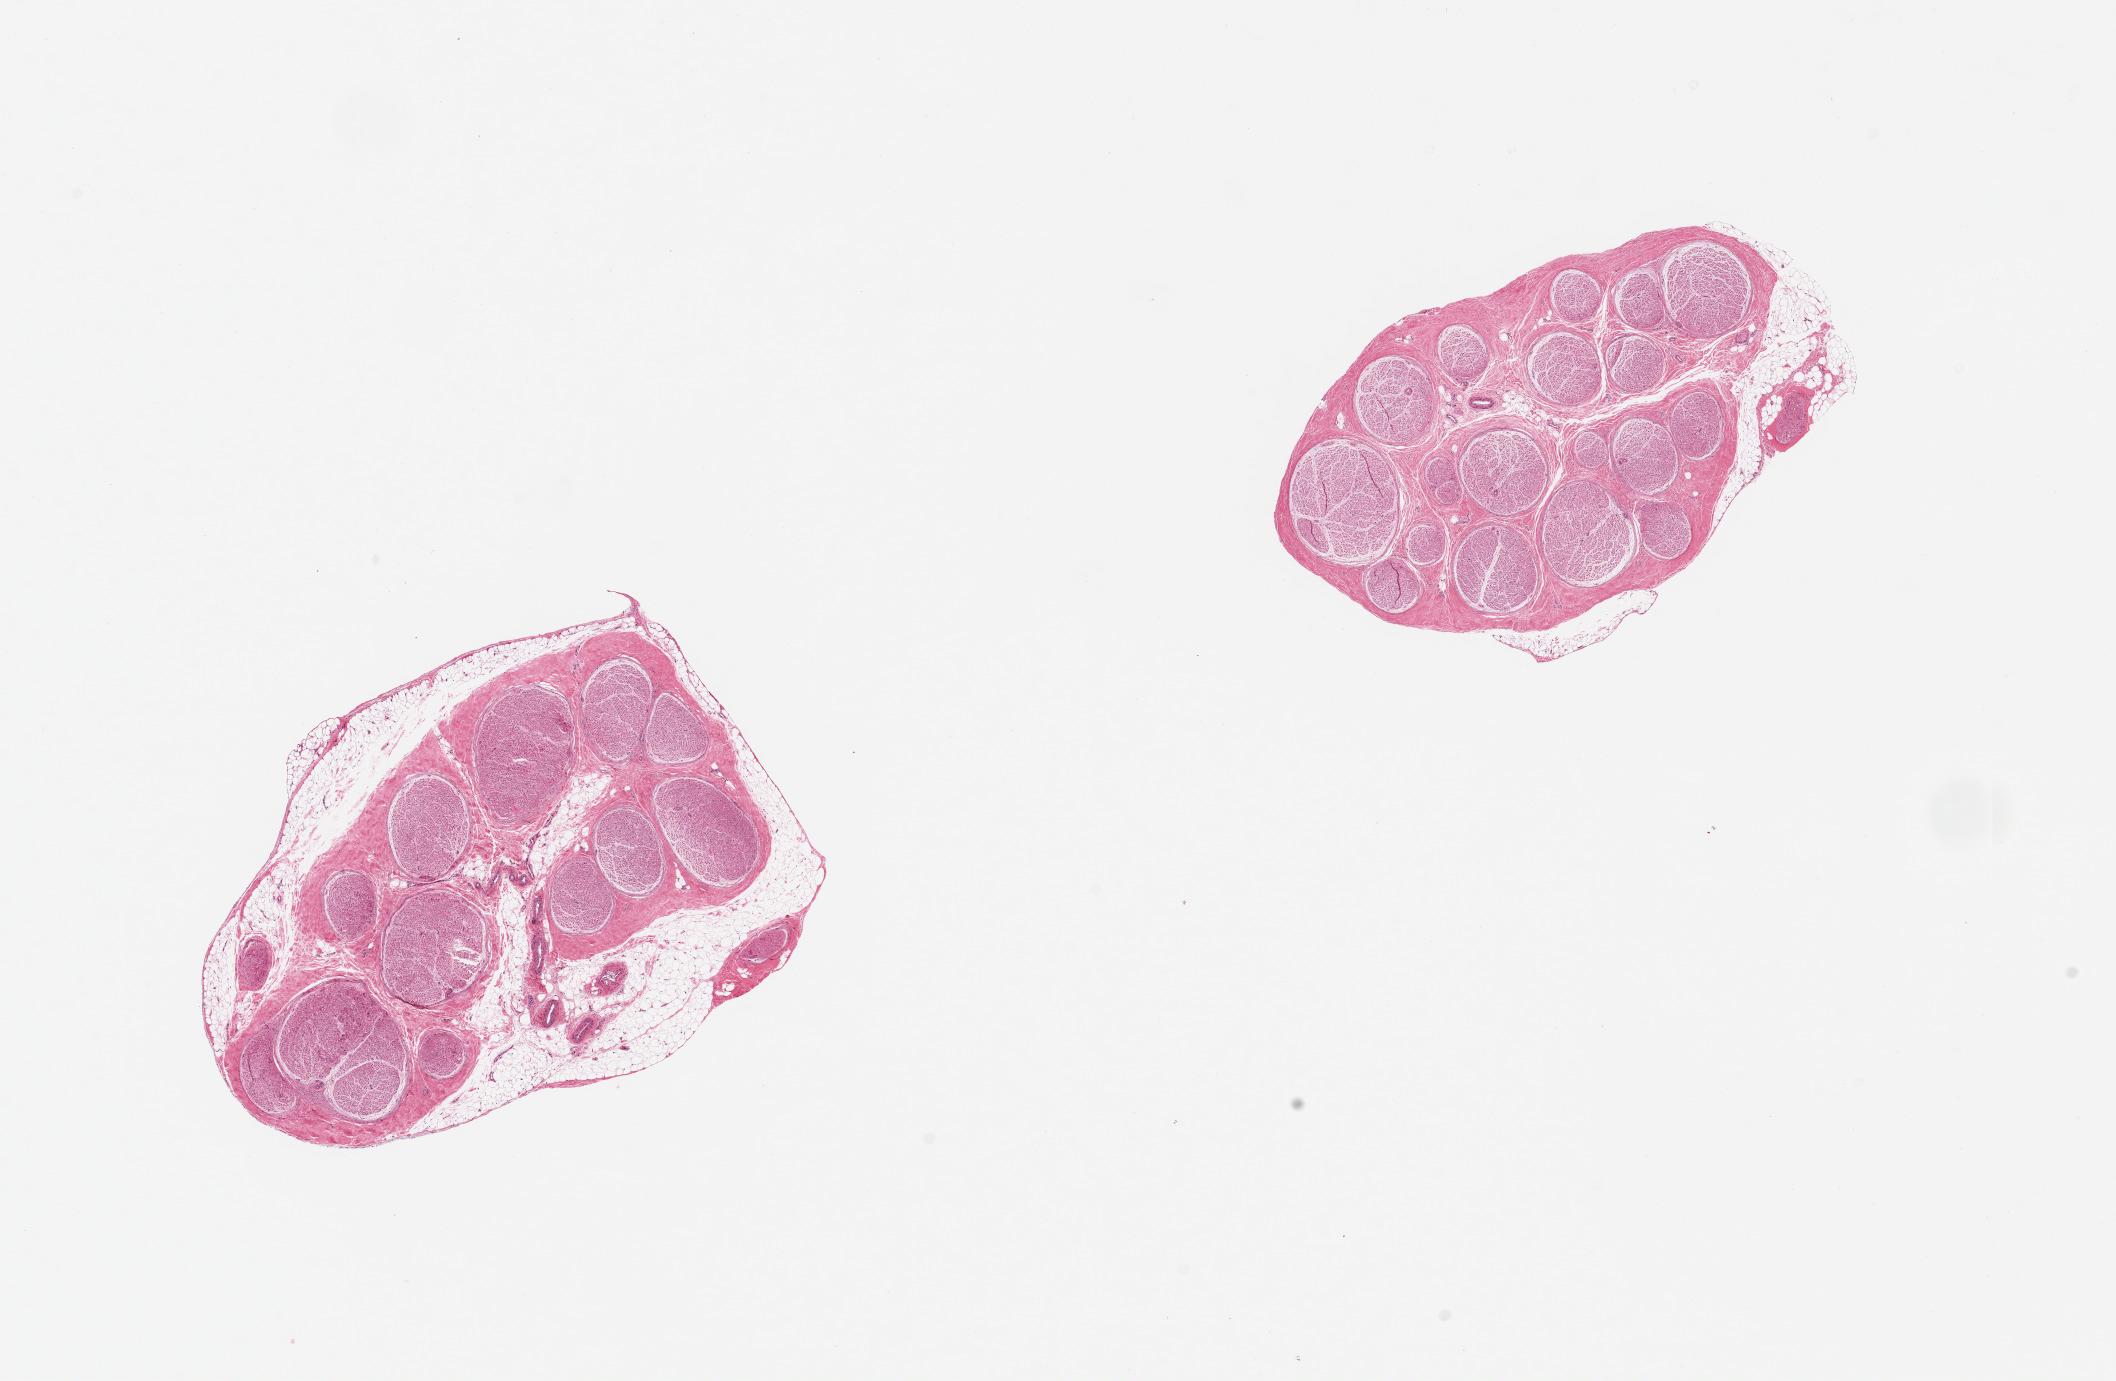
Digitized H&E-stained section, brightfield — low-resolution overview of the scanned area, about 16.7 x 10.9 mm (acquisition: 20x scan). PAXgene-fixed, paraffin-embedded tissue. Section of tibial nerve (target tissue). Tissue donor sample. Donor sex: male.
- pathologist's review note for this sample: 2 pieces, partial rim of fat up to ~0.8mm